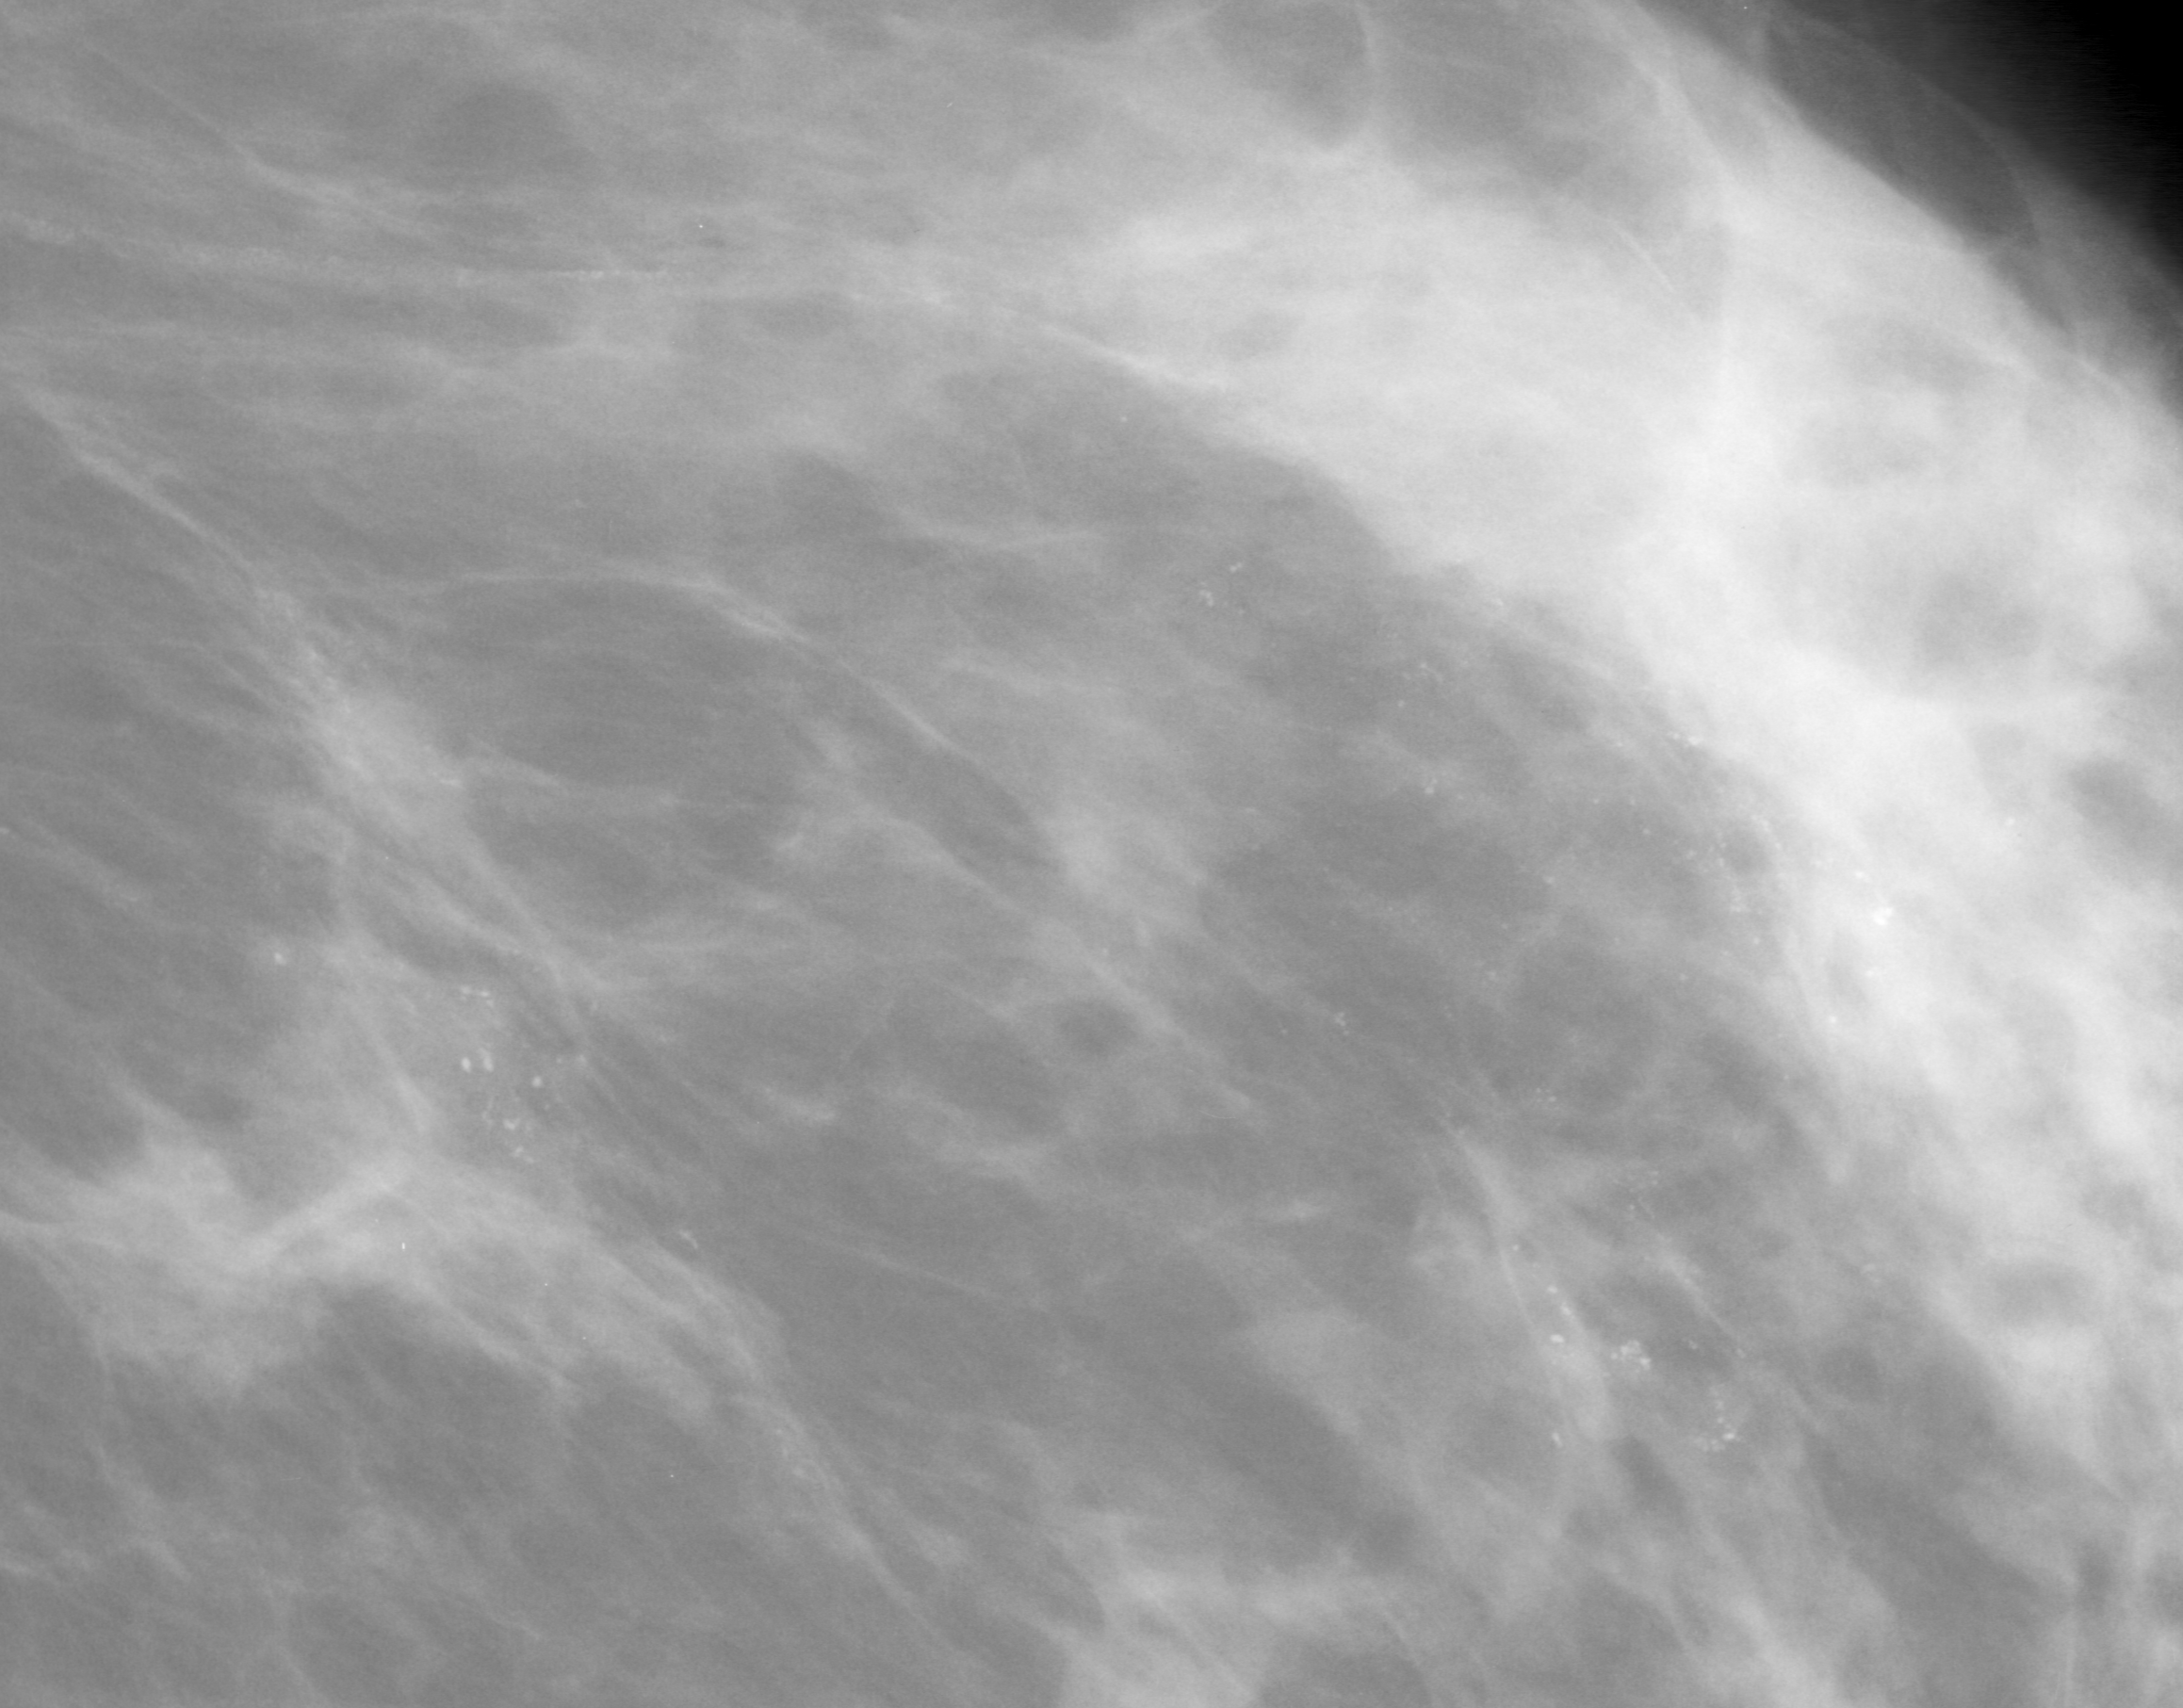
Region of interest cut from a scanned film mammogram (one marked finding); left breast; MLO view; BI-RADS breast density category 3 (scale 1–4).
Calcifications, morphology pleomorphic, distribution regional; BI-RADS assessment category 5; subtlety rating 5 on a 1 (subtle) to 5 (obvious) scale; pathology result (as recorded, not read from the image): malignant.